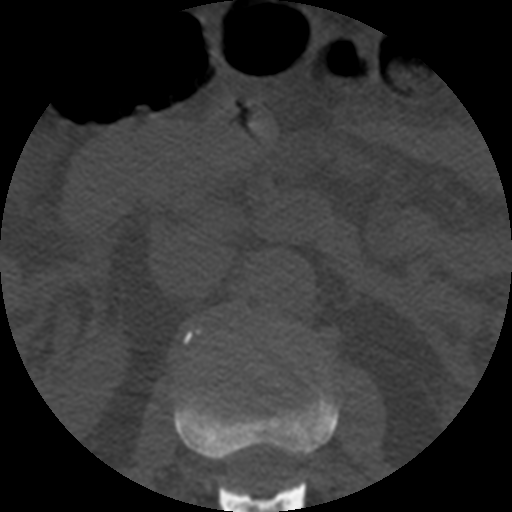
CT including the spine, one axial slice. Position 173 of 508 along the scan axis. Reconstruction kernel STANDARD. 120 kVp. Bone window (W 1800 / L 400 HU). 1.25 mm slice thickness. 512 × 512 image matrix, field of view 160 × 160 mm. Patient age 57 years. Case-level facts recorded for this patient, not image findings: primary cancer: prostate.
Outlined on this slice (semi-automatic segmentation, software-assisted and operator-edited):
- L1 vertebra: bounding box [x1, y1, x2, y2] px = [174, 394, 339, 512]
- L2 vertebra: [184, 330, 199, 342]